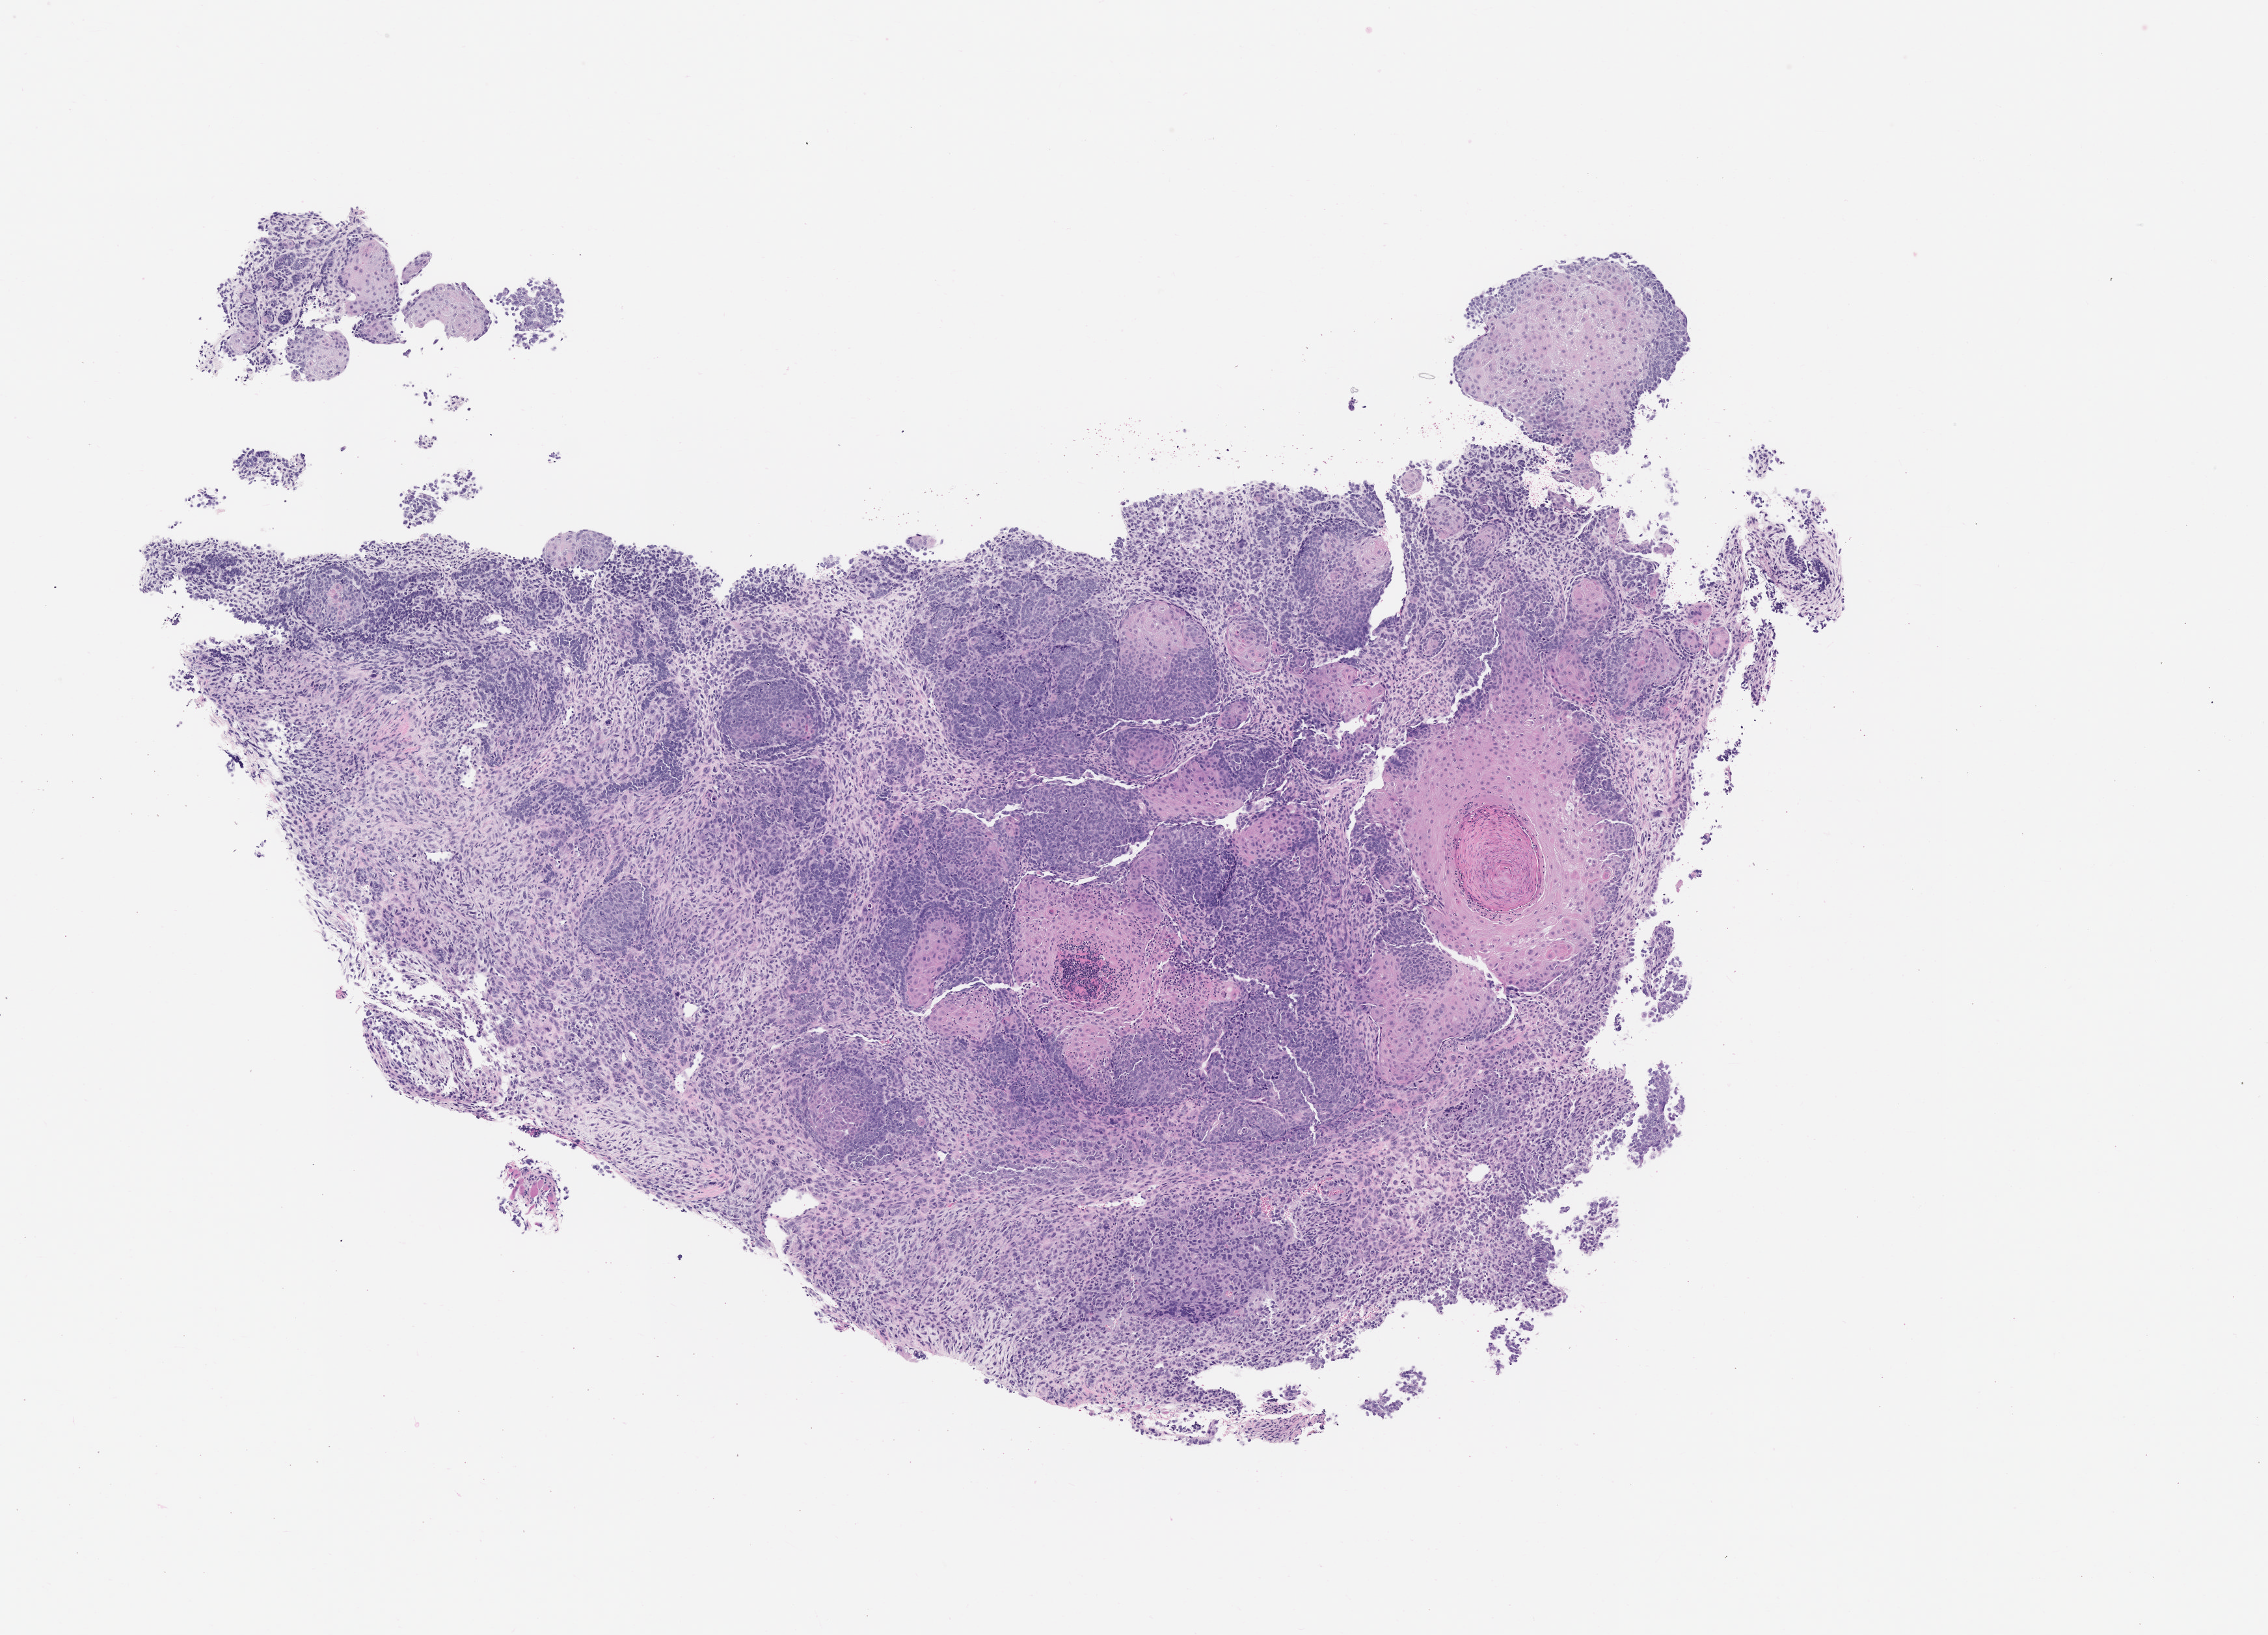
Whole-slide image, H&E: patient-derived xenograft (human tumor grown in a mouse), passage 2 — a low-resolution overview of the entire scanned area, about 7.0 x 5.1 mm. Formalin-fixed, paraffin-embedded (FFPE) tissue. Originating tumor site category: female genital tract.
Originating patient diagnosis: Carcinosarcoma.